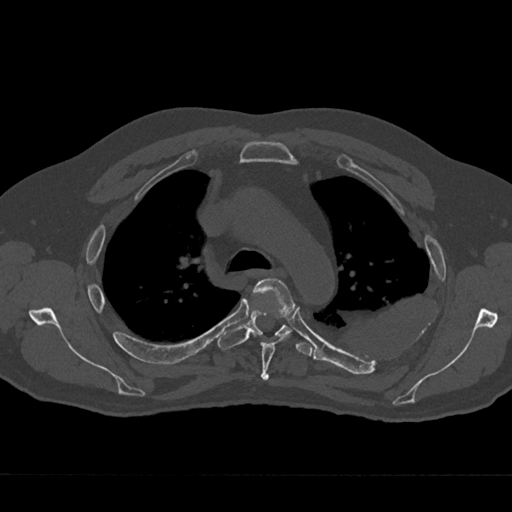
CT including the spine, one axial slice; position 498 of 797 along the scan axis; 120 kVp; bone window (W 1800 / L 400 HU); 512 × 512 image matrix. Patient: male, 75 years. Case-level facts recorded for this patient, not image findings: primary cancer: renal.
Outlined on this slice (semi-automatically segmented with operator editing):
- T4 vertebra: bounding box <252,278,295,381> (left, top, right, bottom; pixels)
- T5 vertebra: <218,309,313,356>